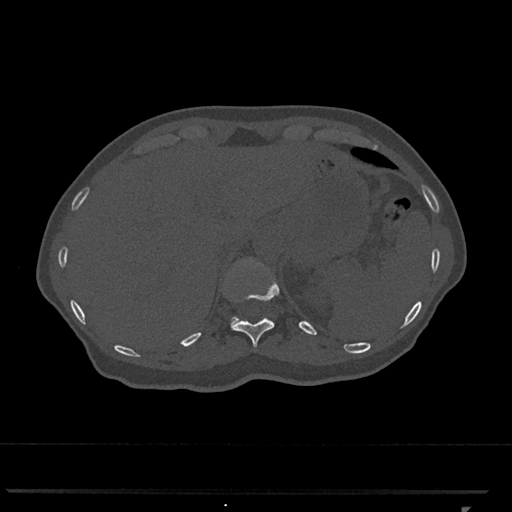
CT including the spine, one axial slice; slice 504 of 793 in the series (ordered by position); reconstruction kernel Br40s/3; 120 kVp; bone window (W 1800 / L 400 HU); 512 × 512 image matrix, field of view 380 × 380 mm. Patient: female, 62 years. From the clinical record (not read from this slice): primary cancer: renal.
Outlined on this slice (semi-automatic segmentation, software-assisted and operator-edited):
- T11 vertebra: bounding box (x1, y1, x2, y2) in pixels: (231, 260, 280, 348)
- T12 vertebra: (231, 317, 271, 325)